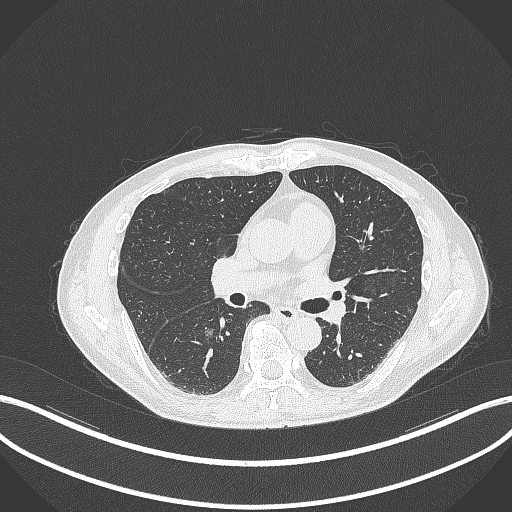
Chest CT, one axial slice; slice 175 of 323 in the series (ordered by position); reconstruction kernel B70f; 120 kVp; lung window (W 1500 / L -600 HU); 1 mm slice thickness; 512 × 512 image matrix. Patient: male, 61 years. Case-level facts recorded for this patient, not image findings: clinical TNM (as recorded): T1c N0 M0.
Outlined on this slice (rectangle marked by the reading radiologist):
- lung tumour (recorded histology: adenocarcinoma): box from (x=201, y=325) to (x=217, y=341) px